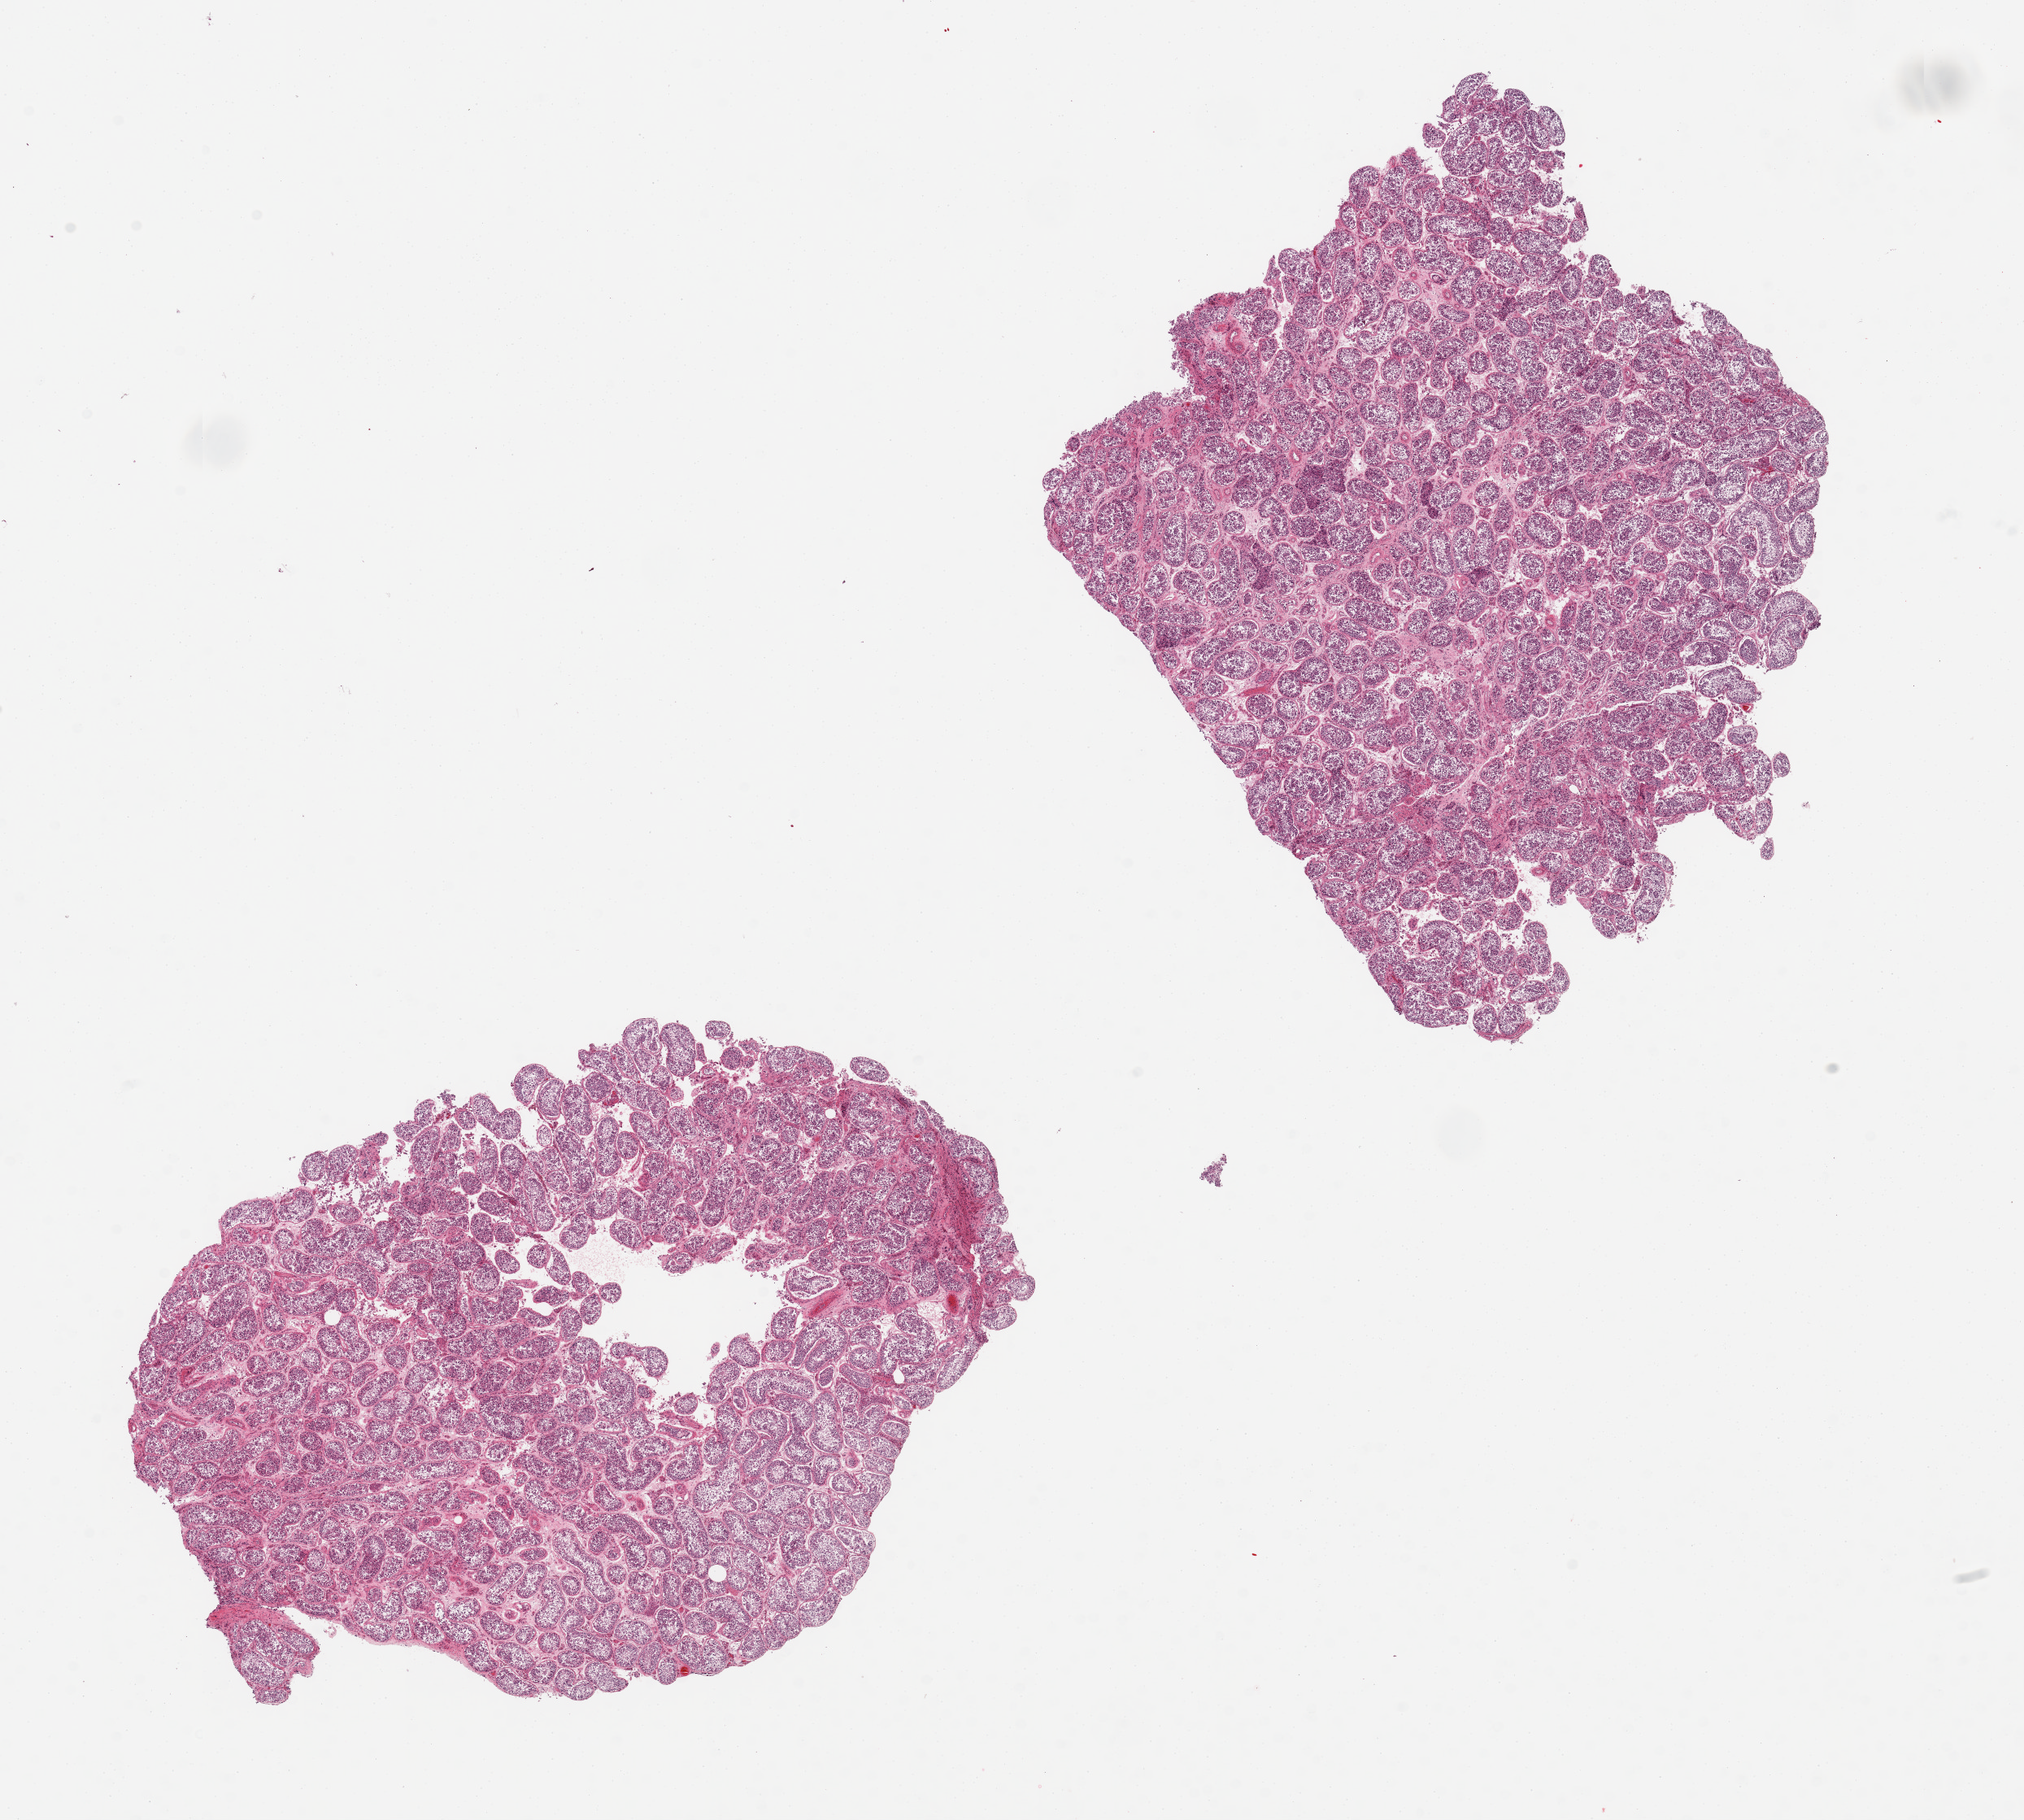
Whole-slide image, hematoxylin and eosin (H&E) stain, brightfield, low-resolution overview of the scanned area, about 19.7 x 17.7 mm (from a 20x scan); PAXgene-fixed paraffin-embedded (PFPE) section; section of testis (target tissue); tissue donor sample.
Pathologist's review note for this sample: 2 pieces; active spermatogenesis.